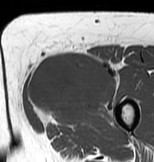
MRI of an extremity soft-tissue mass, one axial slice. MR volume resampled by the dataset authors to the PET/CT grid (not the native acquisition matrix). 3.27 mm slice thickness. 154 × 162 image matrix, field of view 150 × 158 mm. Female patient. From the clinical record (not read from this slice): histological type: myxofibrosarcoma; grade: intermediate; site of the primary tumour: left thigh.
Annotated regions visible in this slice (expert contour drawn on MRI and transferred to this co-registered scan by the dataset authors):
- gross tumour volume including surrounding oedema: bounding box <26,52,120,126> (left, top, right, bottom; pixels)
- gross tumour volume (mass): <28,52,116,117>